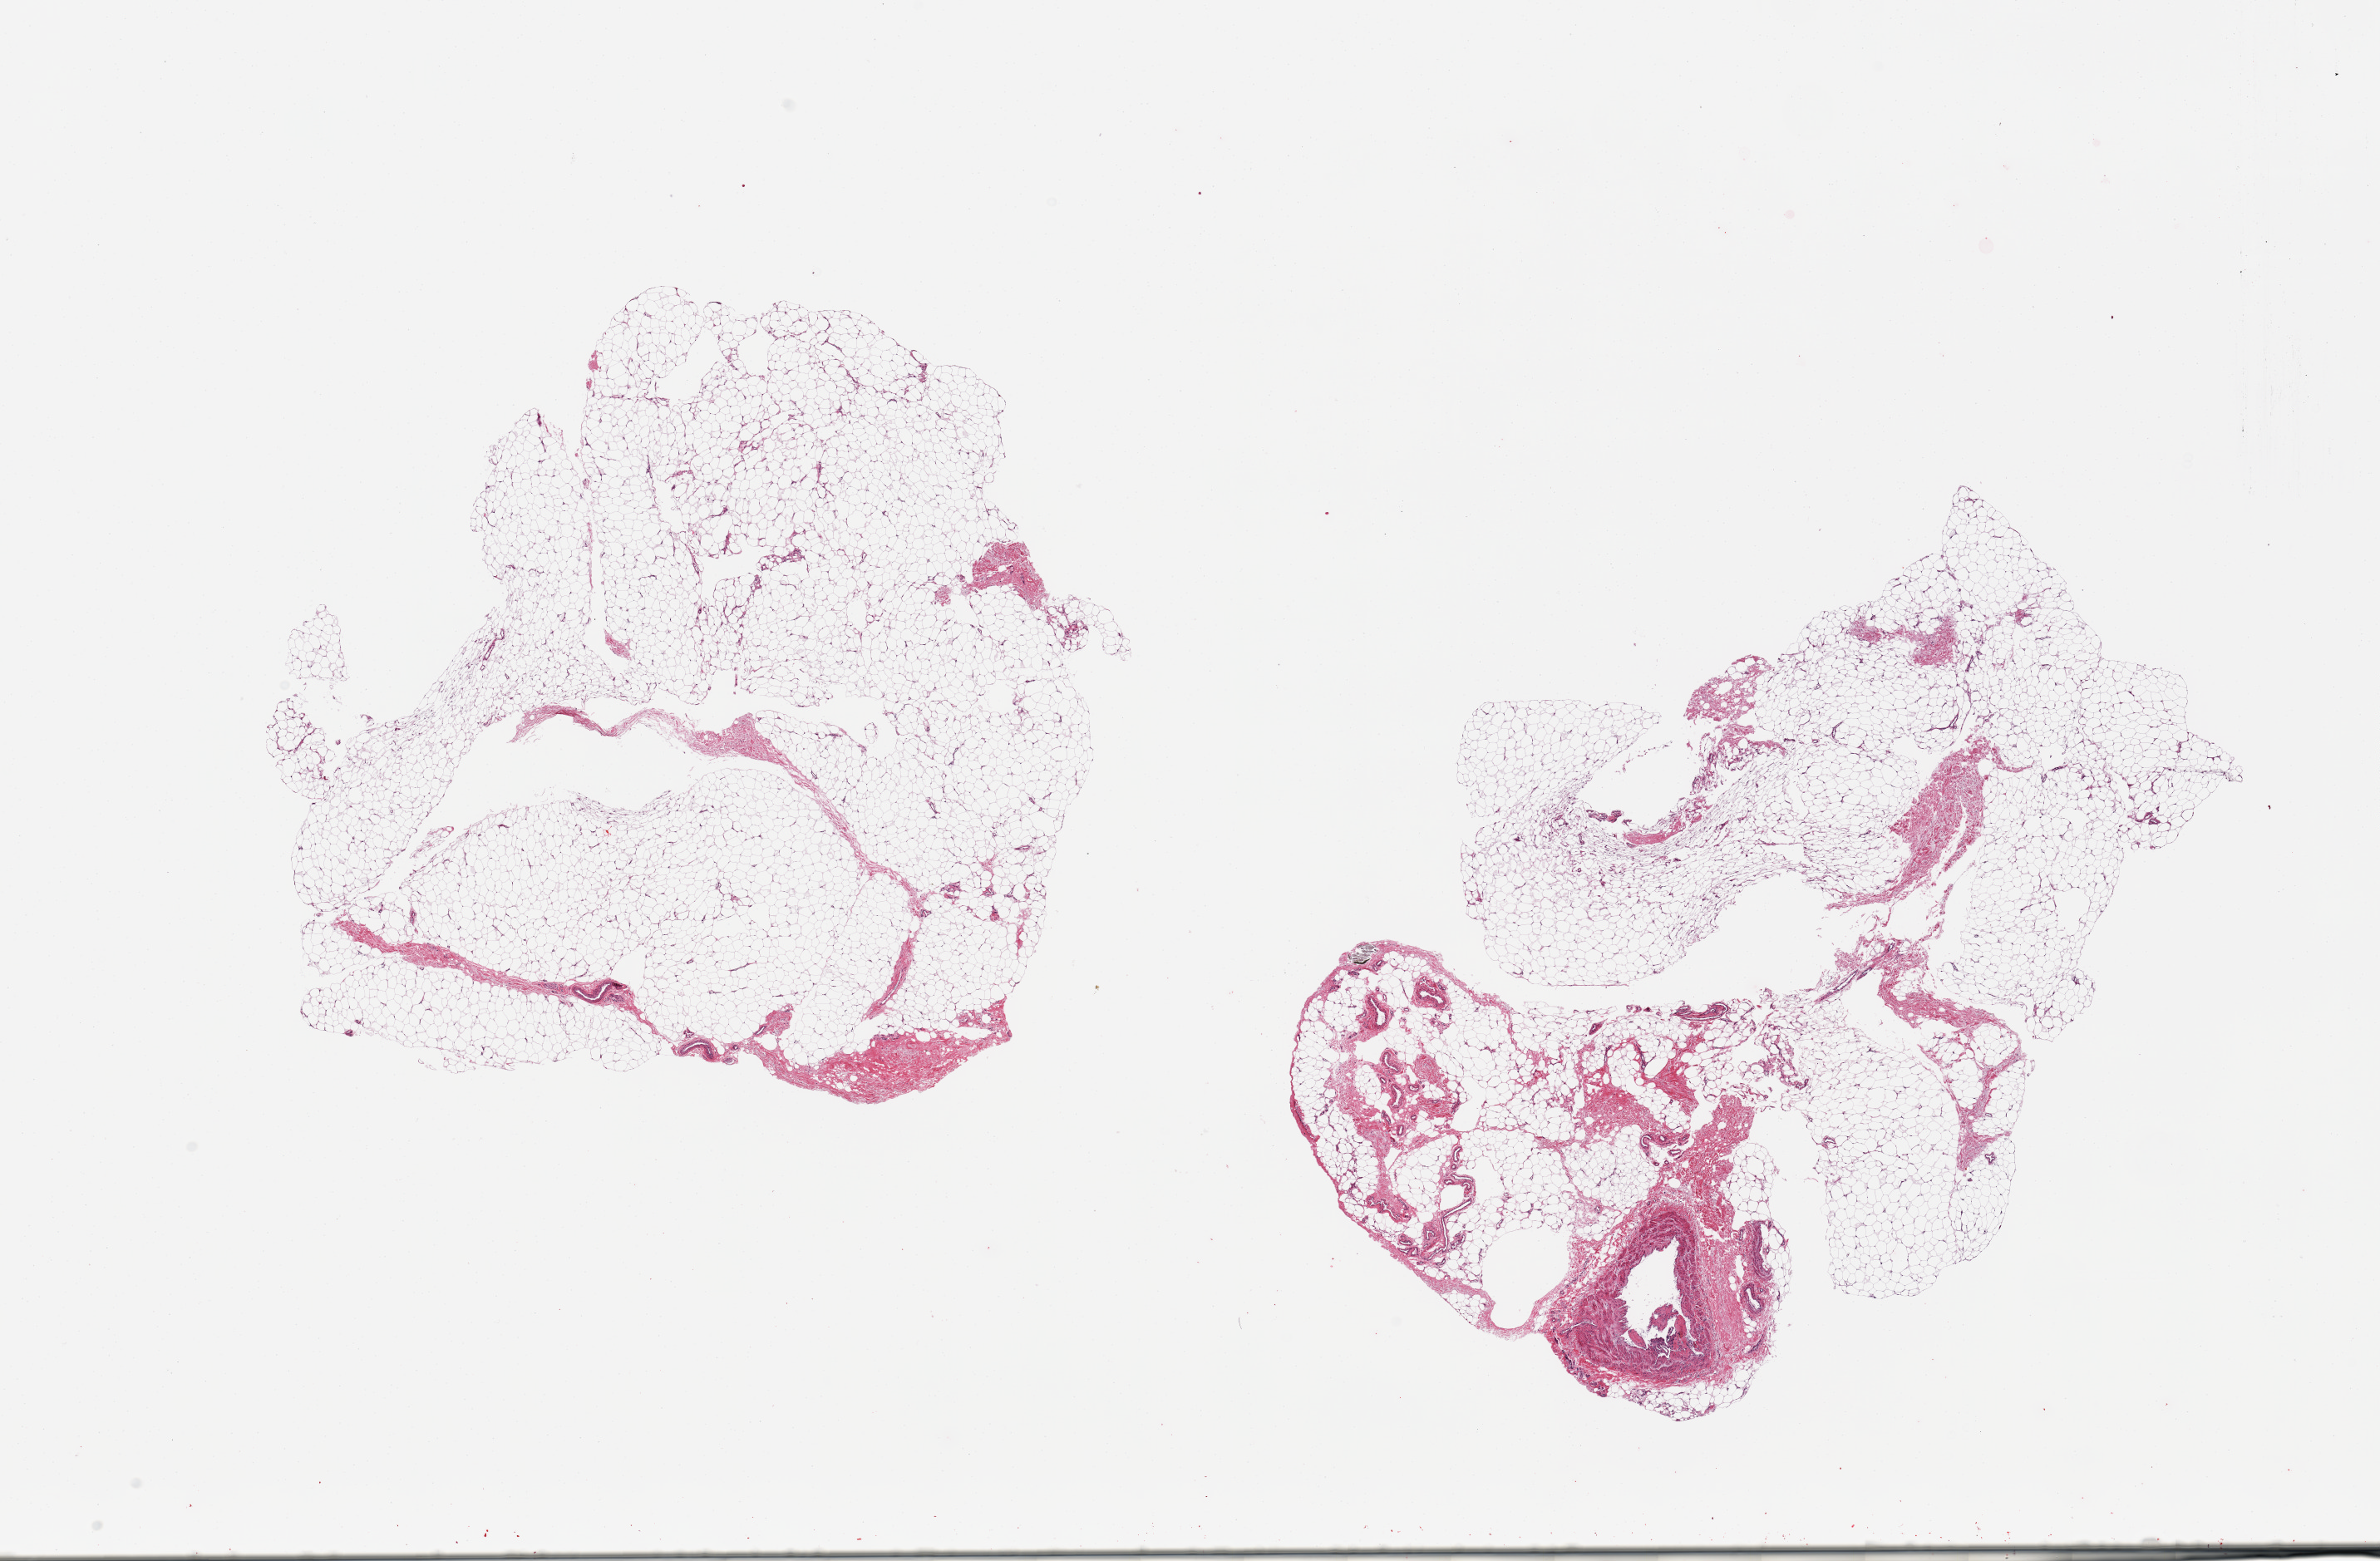
Whole-slide image, haematoxylin and eosin stain — a low-resolution overview of the entire scanned area, about 22.6 x 14.9 mm; PAXgene-fixed, paraffin-embedded tissue; sampled site (target tissue): adipose tissue; donor tissue sample. Donor: female.
Pathologist's review note for this sample: 2 pieces, fascia/vascular elements are ~10% of tissue.